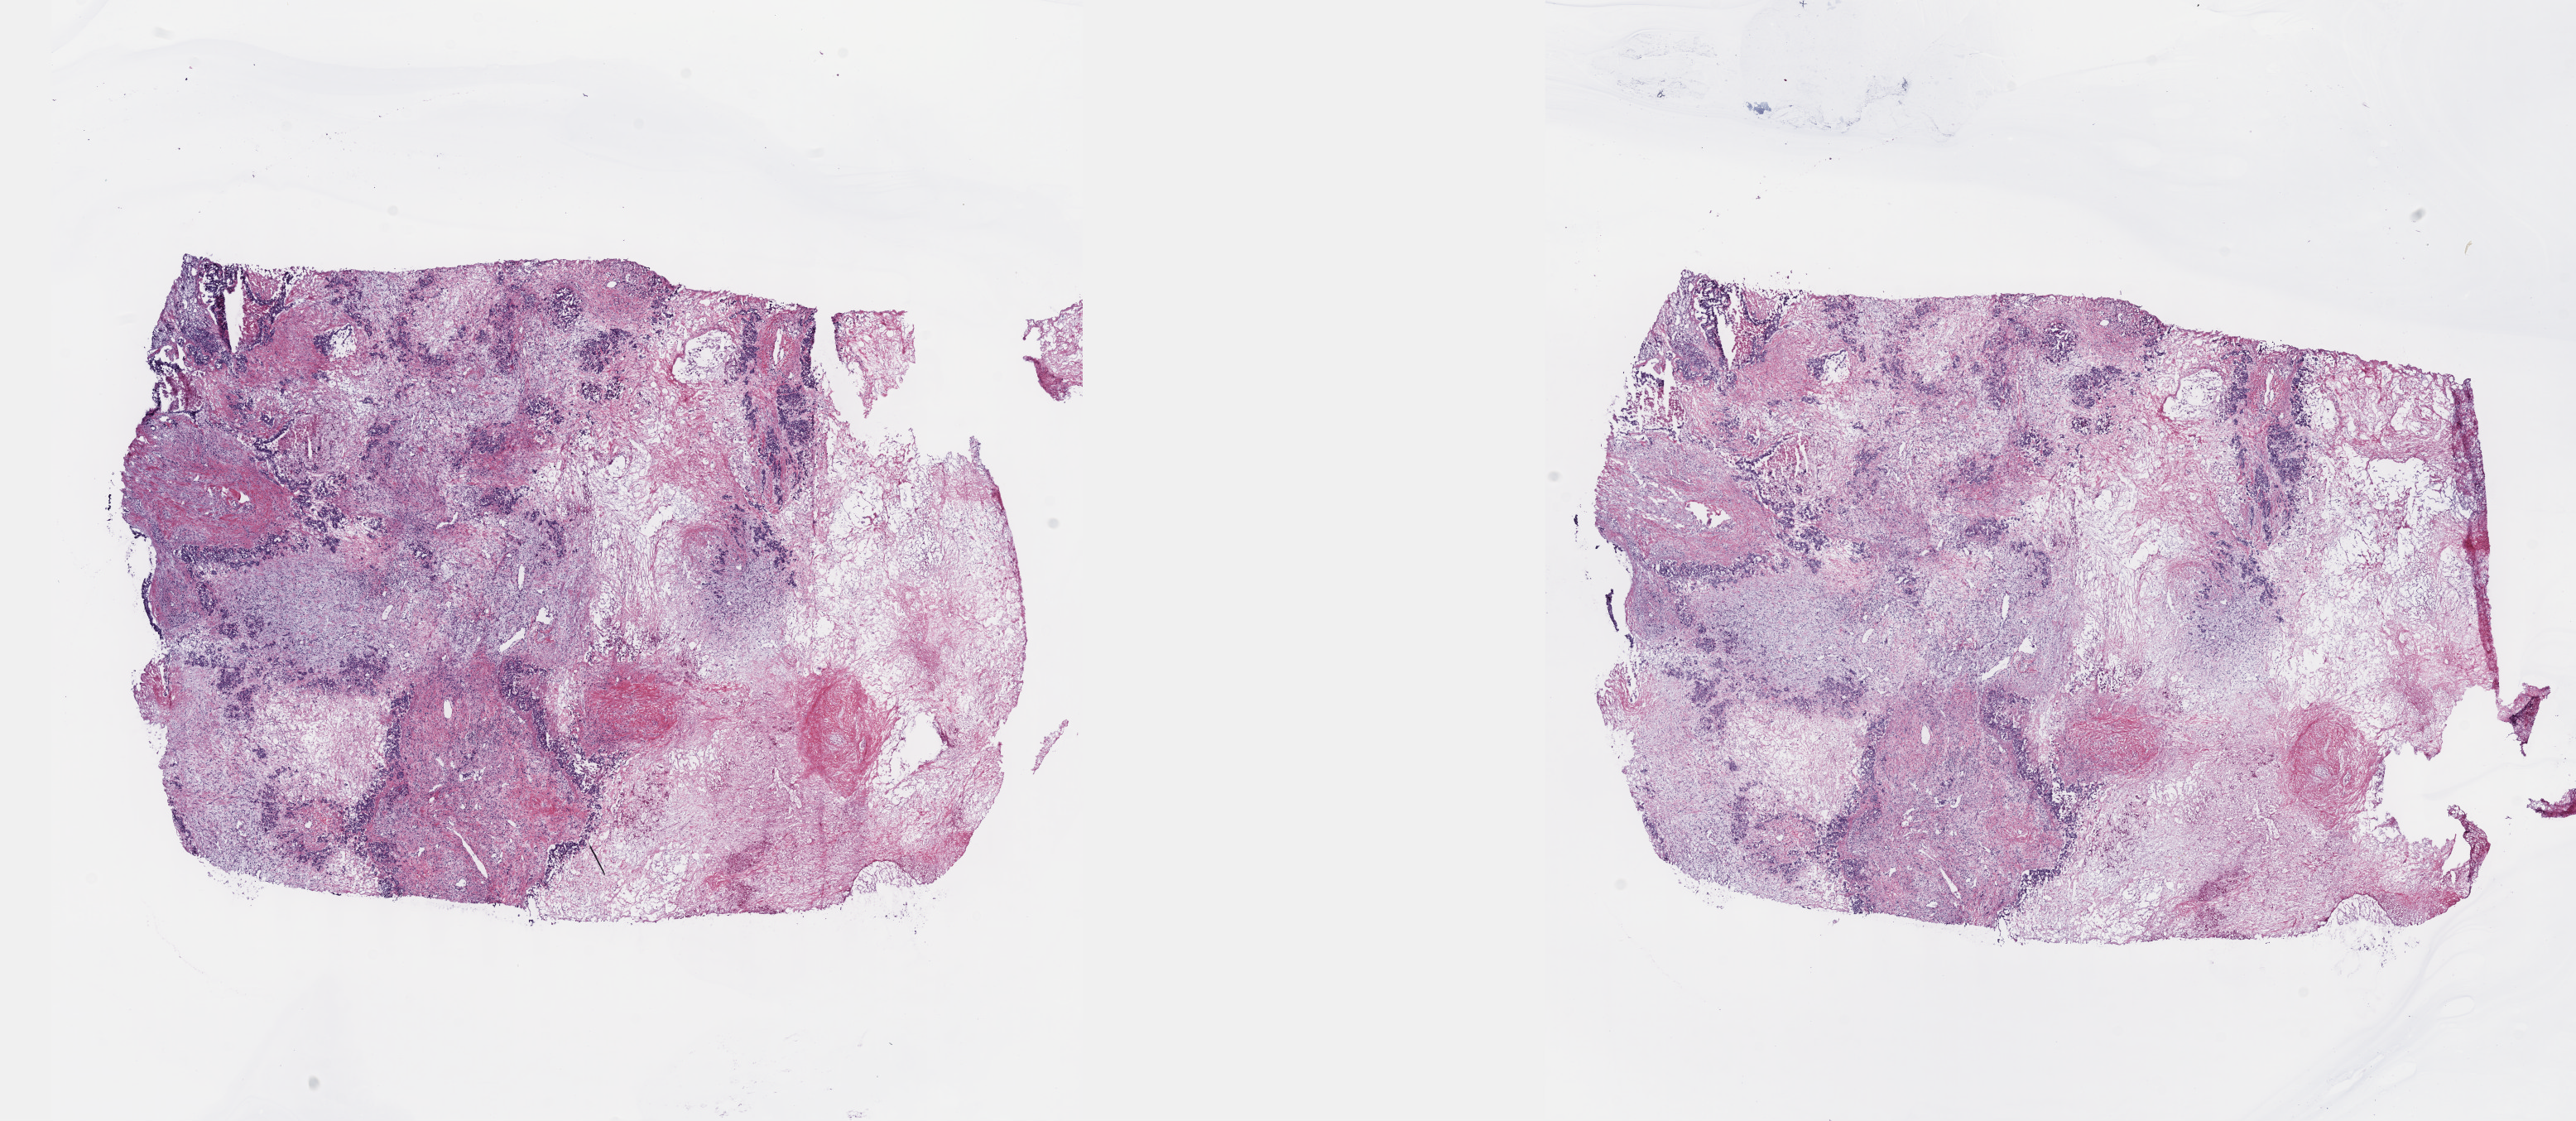
Whole-slide histology image, H&E-stained, low-resolution overview of the scanned area, about 25.1 x 10.9 mm (acquisition: 40x scan). Frozen section. Primary tumour sample from the bile duct. Male, age 59 years at initial diagnosis. Histologic grade: G3 (poorly differentiated). Composition of this section per pathologist review: tumour cells 95%, tumour nuclei 65%, normal cells 0%, stromal cells 0%, necrosis 5%. Infiltration values recorded for this section: lymphocyte infiltration 3%, monocyte infiltration 2%, neutrophil infiltration 3%.
AJCC pathologic stage: IVB (7th edition). Histologic diagnosis: Cholangiocarcinoma.